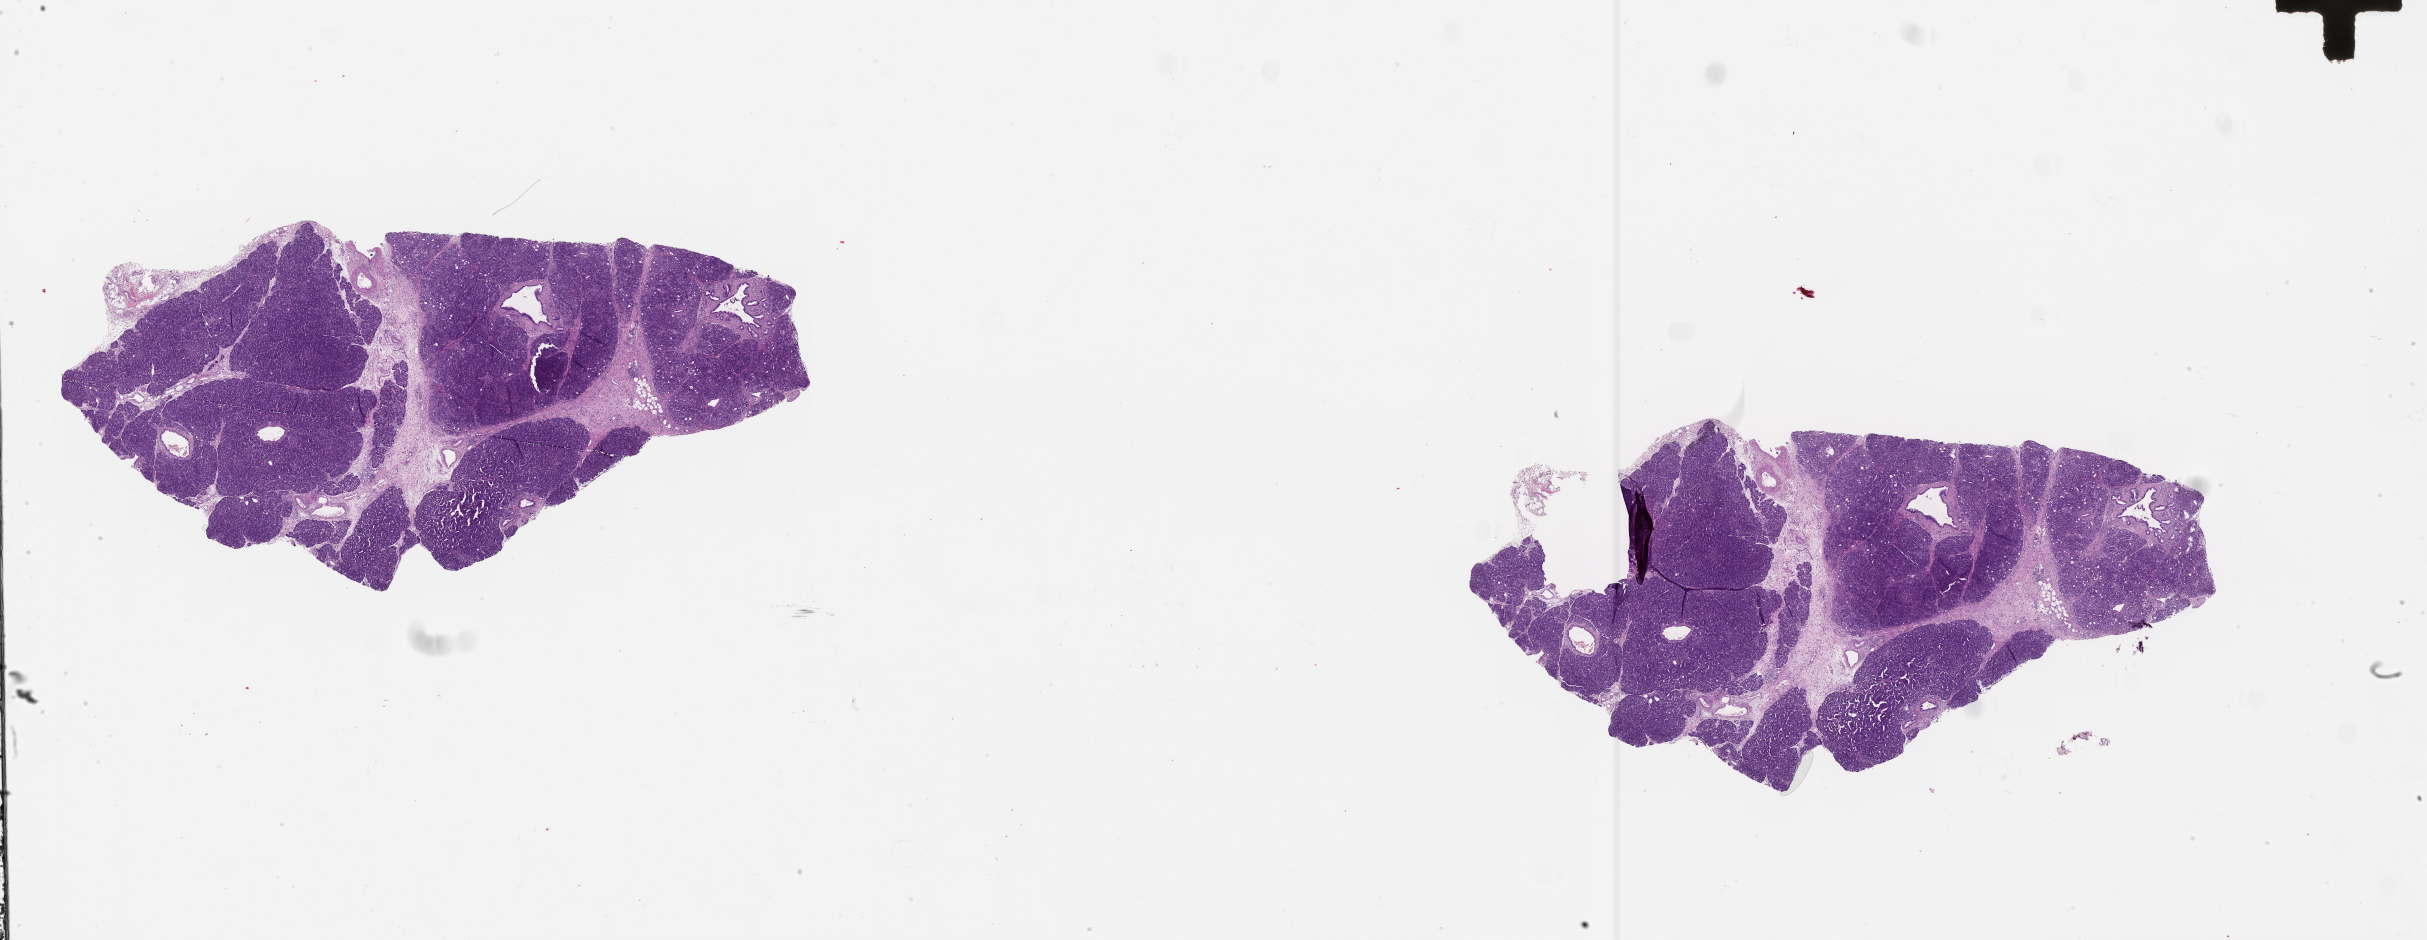
Digitized Hematoxylin and eosin (H&E) stained tissue section (whole slide) — whole scanned area (about 39.1 x 15.1 mm, from a 20x scan) shown as a low-resolution overview; tumour tissue sample, pancreas. Patient: male, age 69 years. Histologic grade: G2 (moderately differentiated).
Histologic diagnosis: Infiltrating duct carcinoma, NOS. Primary tumour site (as recorded): head. AJCC pathologic stage: IA.